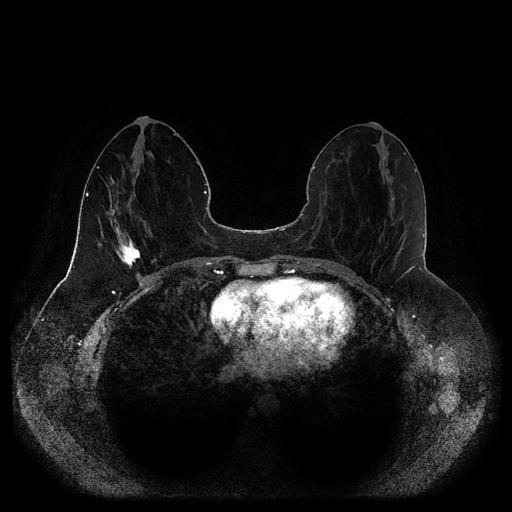
Breast MRI (dynamic contrast-enhanced, multi-phase), one axial slice; position 41 of 116 along the scan axis; dynamic contrast-enhanced series, time point 2 of 5 at this slice position (early post-contrast); 1.5 T; TE 2.5 ms, TR 5.2 ms; 2 mm slice thickness; 512 × 512 image matrix, field of view 390 × 390 mm. Patient: female, 44 years.
Outlined on this slice (semi-automatically segmented with operator editing):
- breast lesion (labelled 'tumour' in the annotation; benign lesions carry a separate 'benign' label): bounding box (x1, y1, x2, y2) in pixels: (113, 237, 140, 270)
- breast lesion (labelled 'tumour' in the annotation; benign lesions carry a separate 'benign' label): (99, 175, 120, 239)